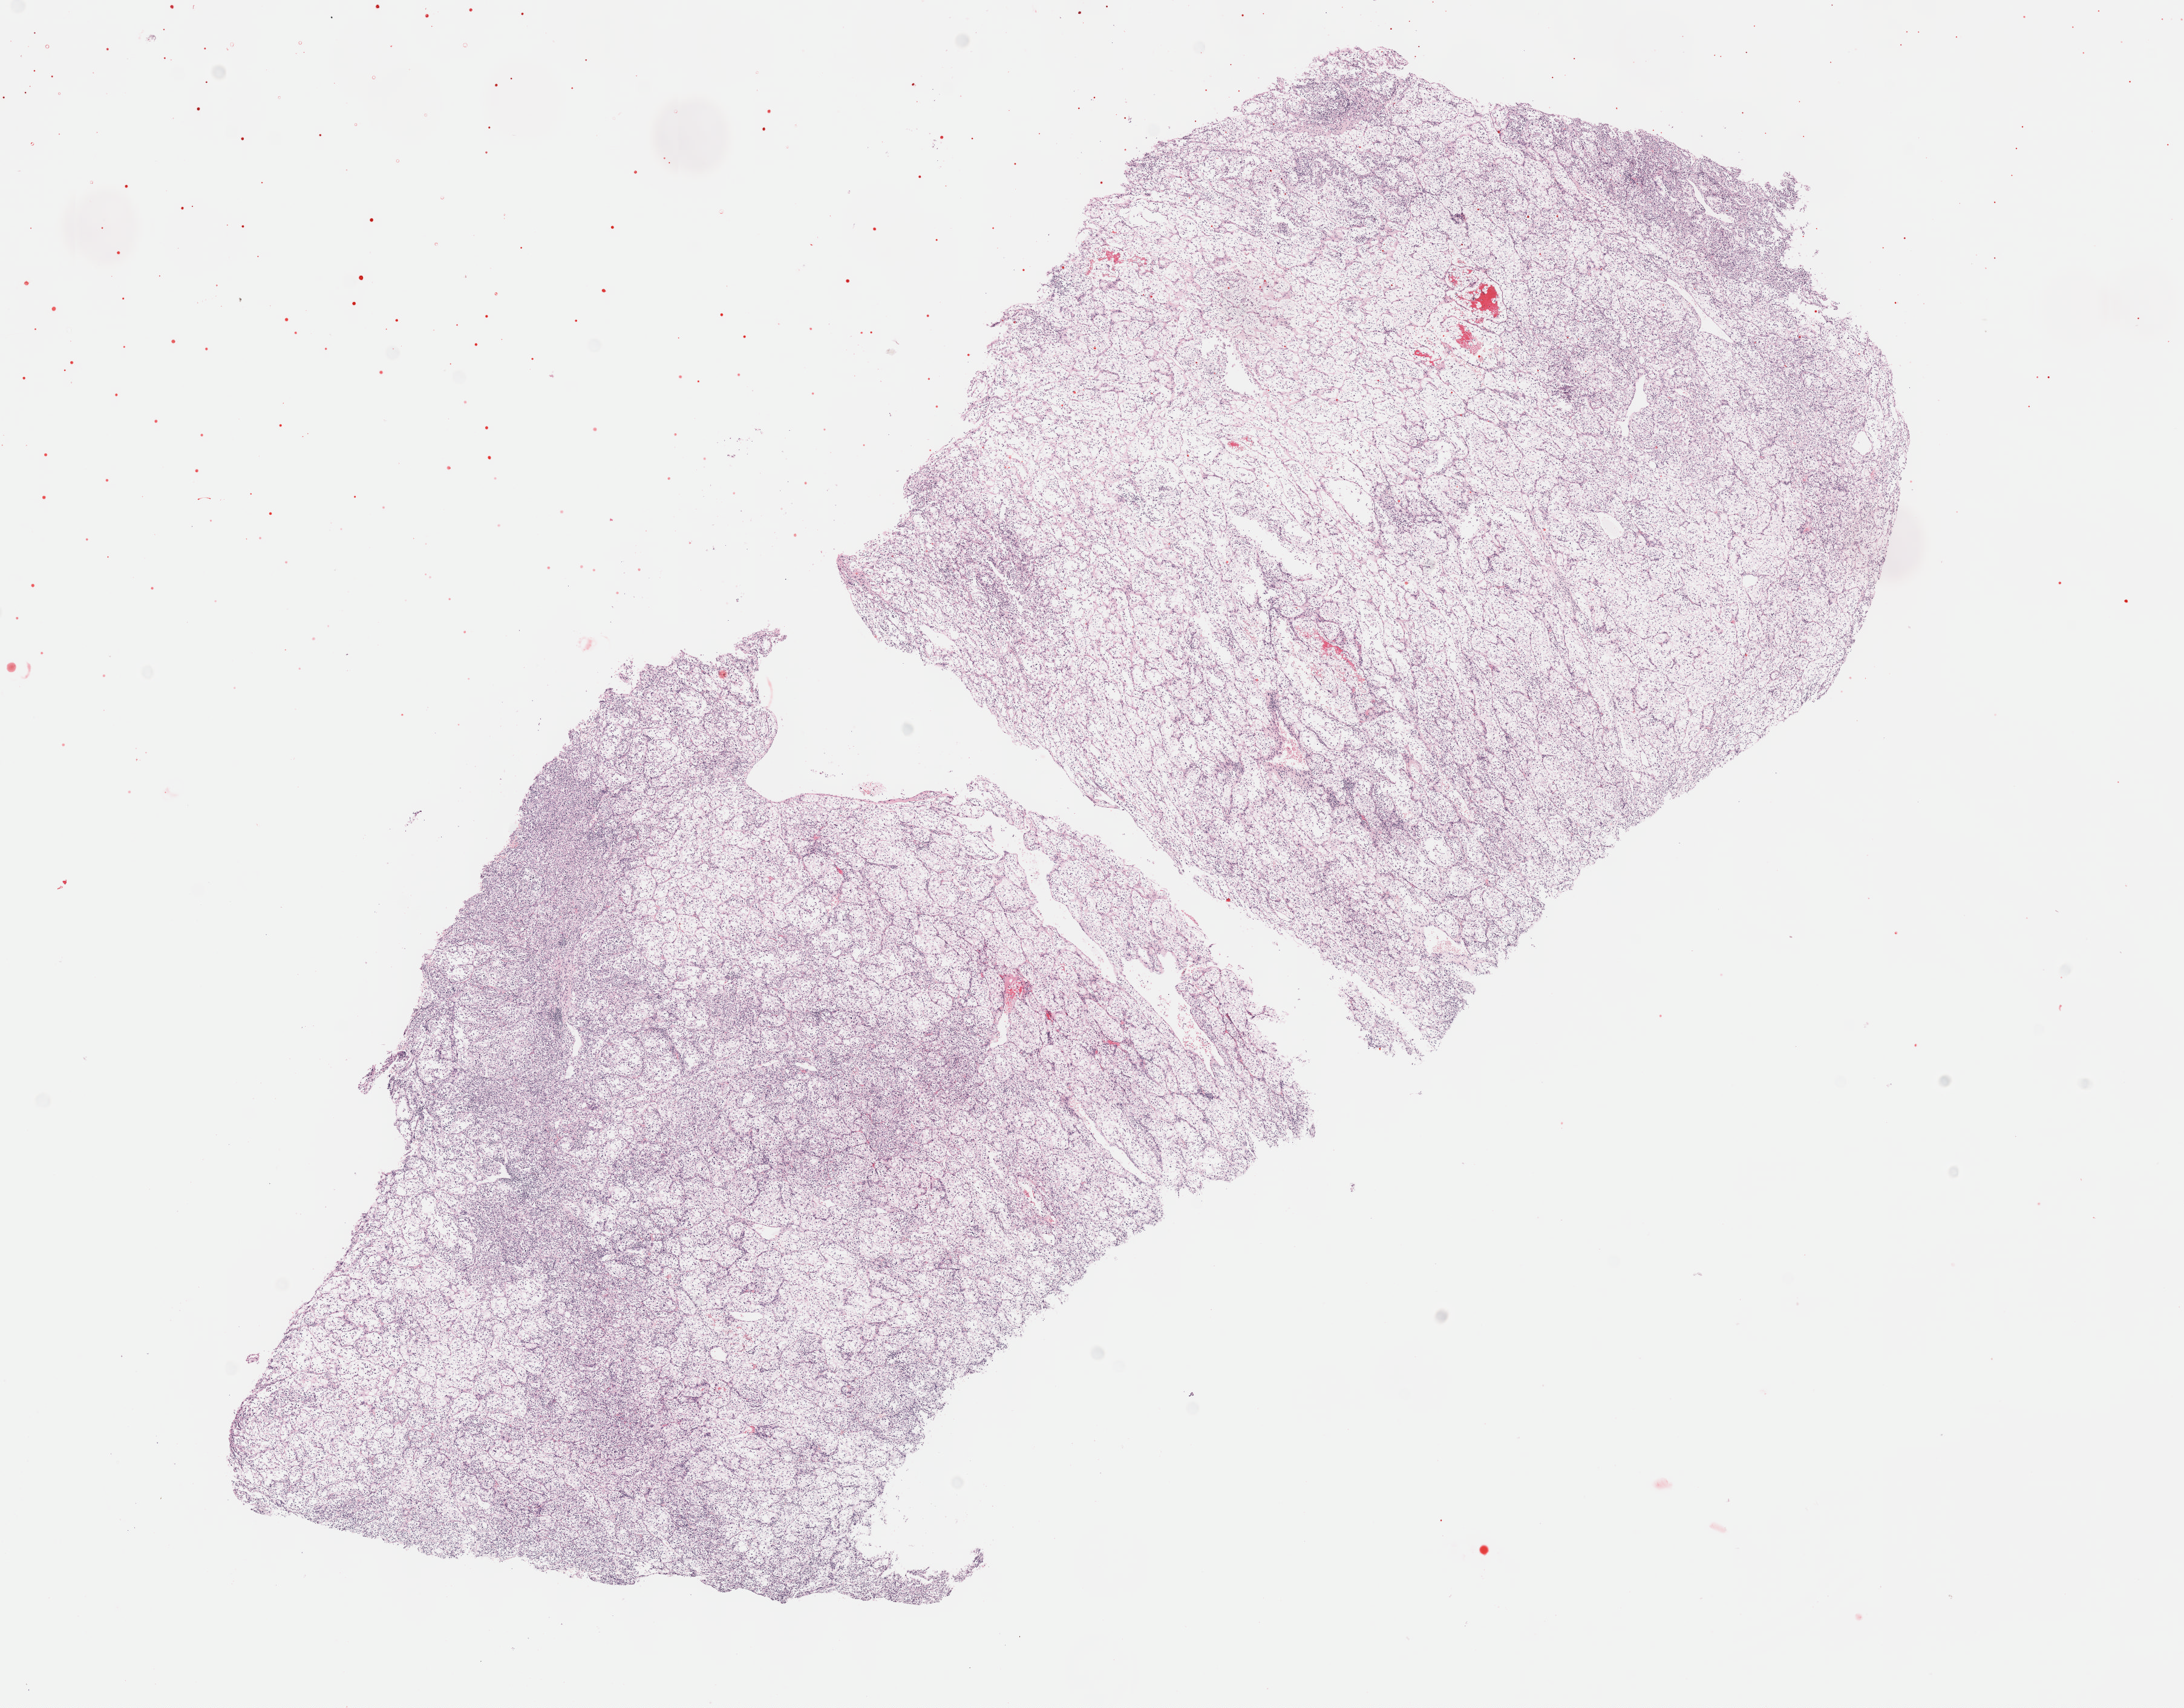
Whole-slide histology image, H&E-stained, shown as a low-resolution overview of the whole scanned area (about 14.6 x 11.4 mm); formalin-fixed paraffin-embedded (FFPE) diagnostic section; kidney, primary tumour sample. Female, age 71 years at initial diagnosis. Histologic grade: G3 (poorly differentiated).
• diagnosis: Clear cell adenocarcinoma, NOS
• laterality: right
• AJCC pathologic stage: III